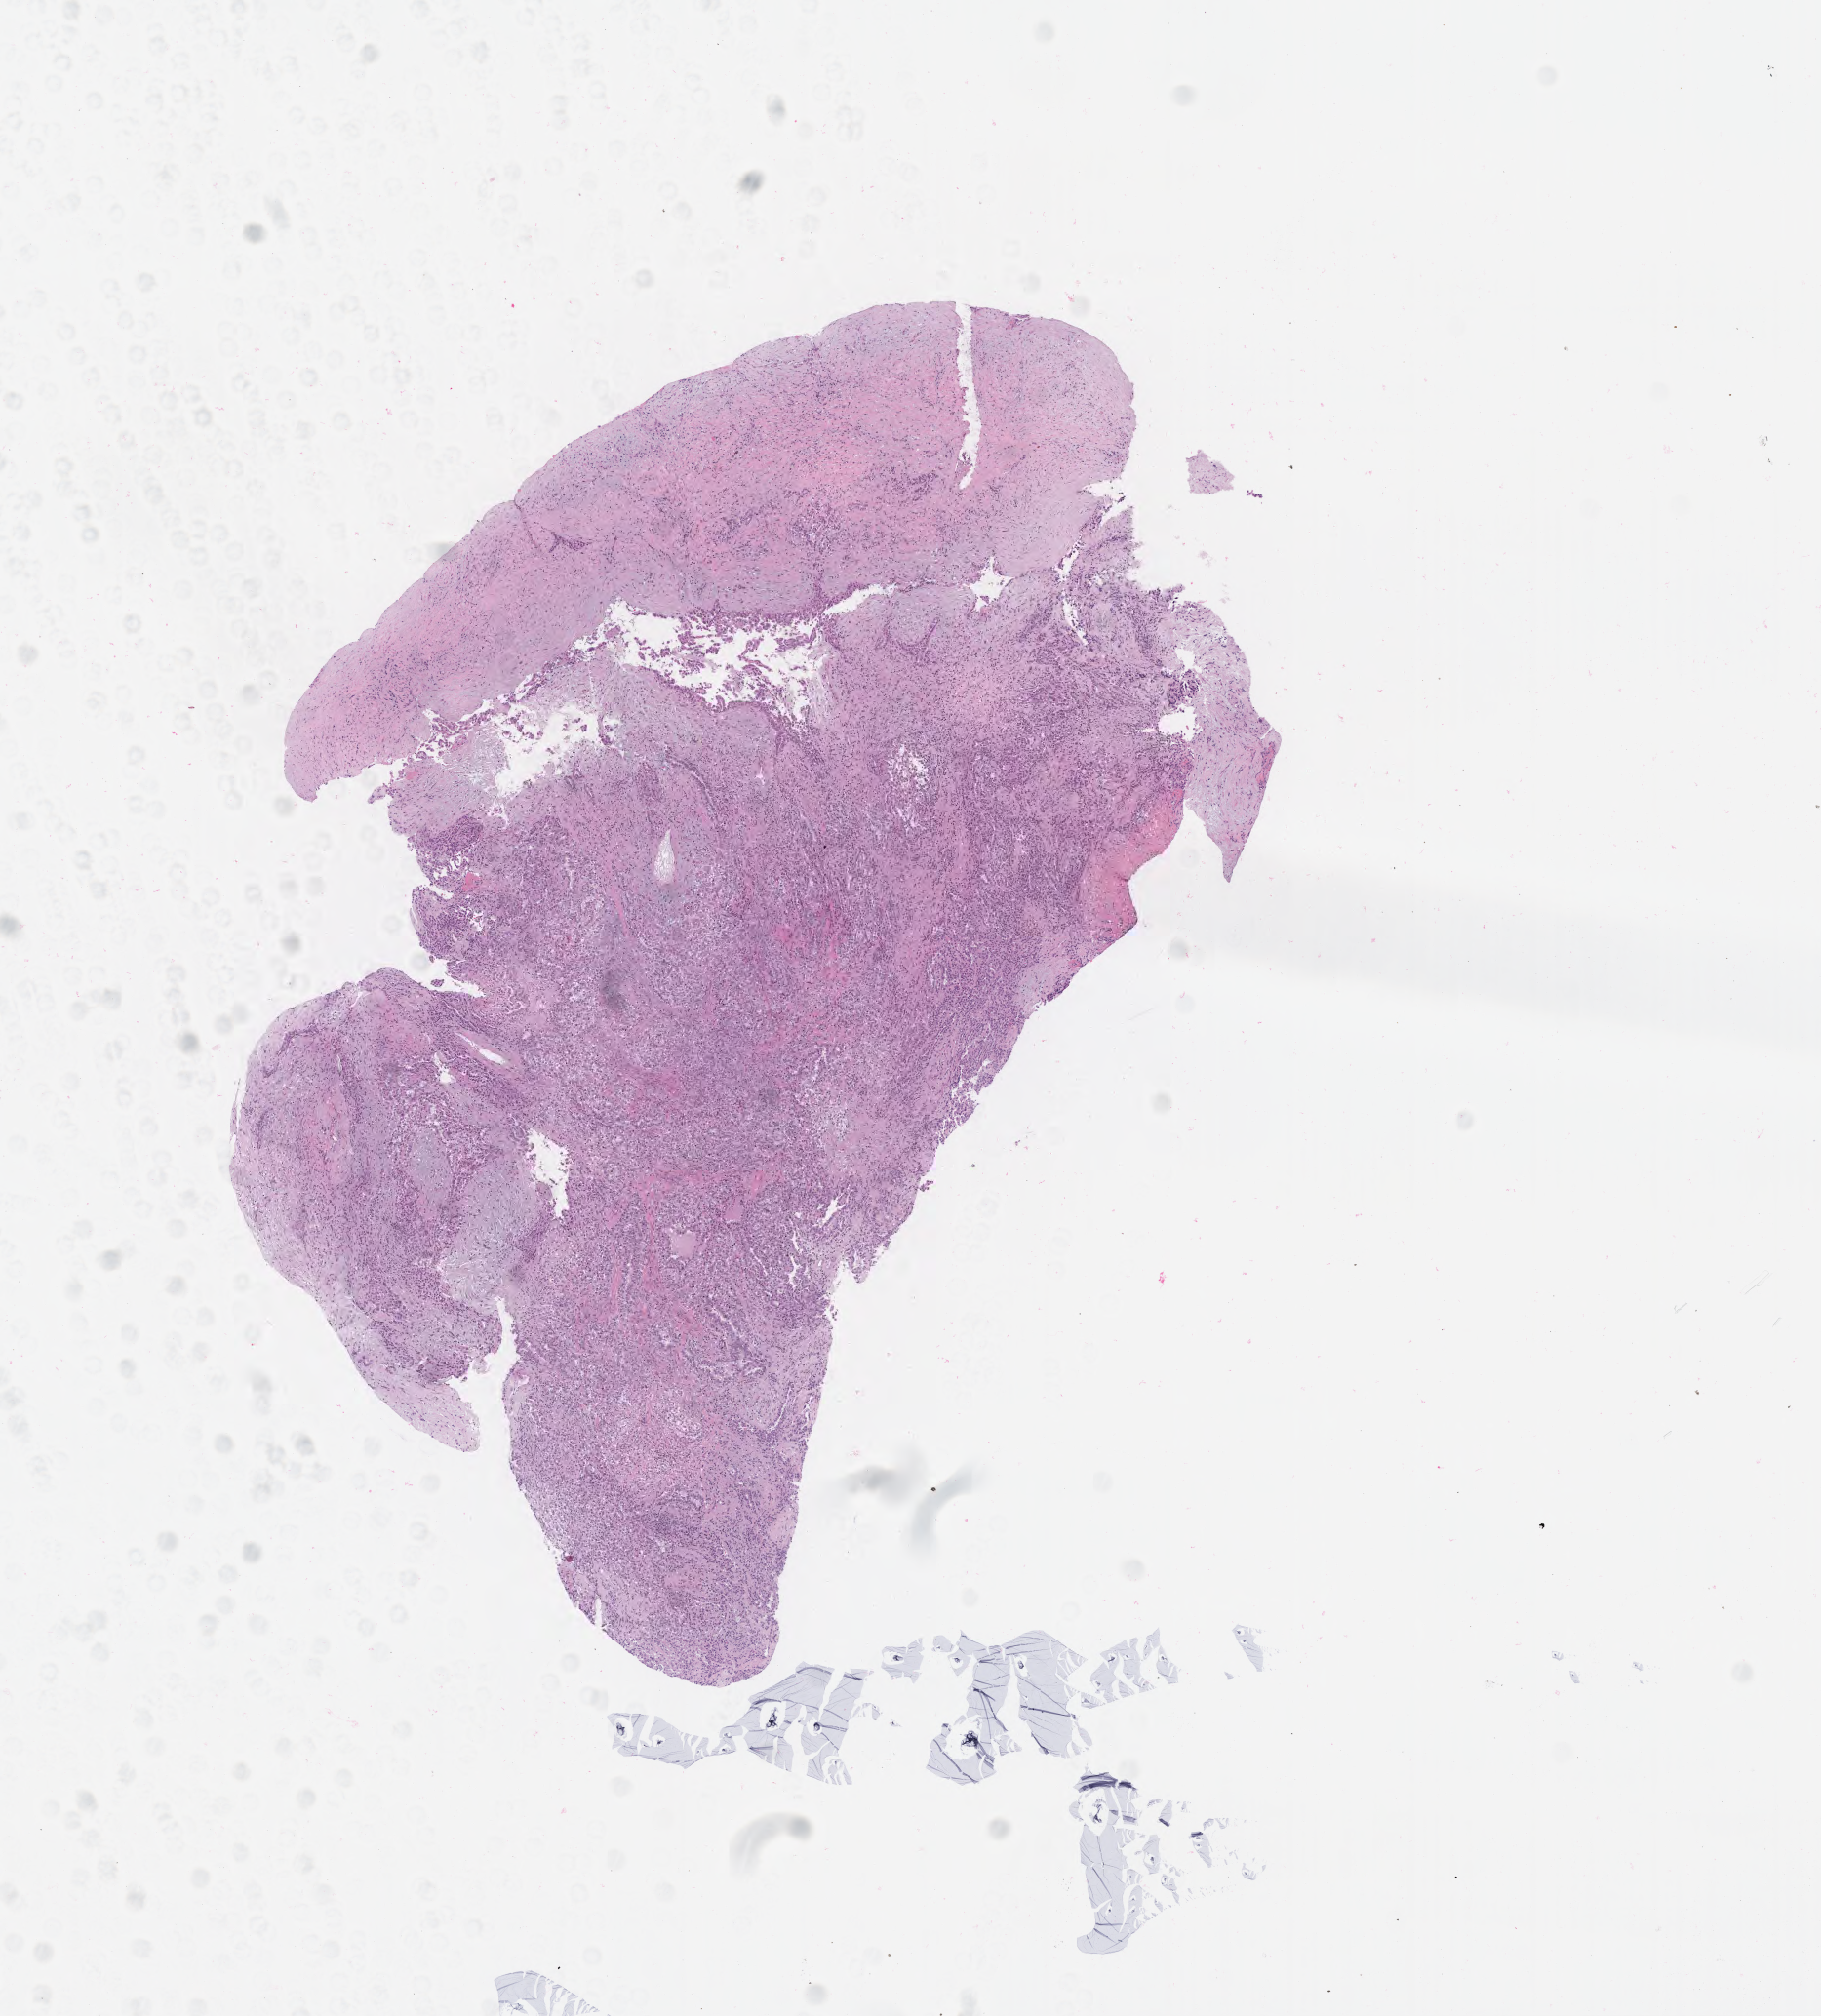
Hematoxylin and eosin (H&E) stained whole-slide image — whole scanned area (about 7.5 x 8.4 mm, acquisition: 40x scan) shown as a low-resolution overview, formalin-fixed paraffin-embedded (FFPE) diagnostic section, sample: primary tumour, mesothelium. Female patient; age at initial diagnosis 53 years.
Diagnosis: Epithelioid mesothelioma, malignant (pleura, NOS).